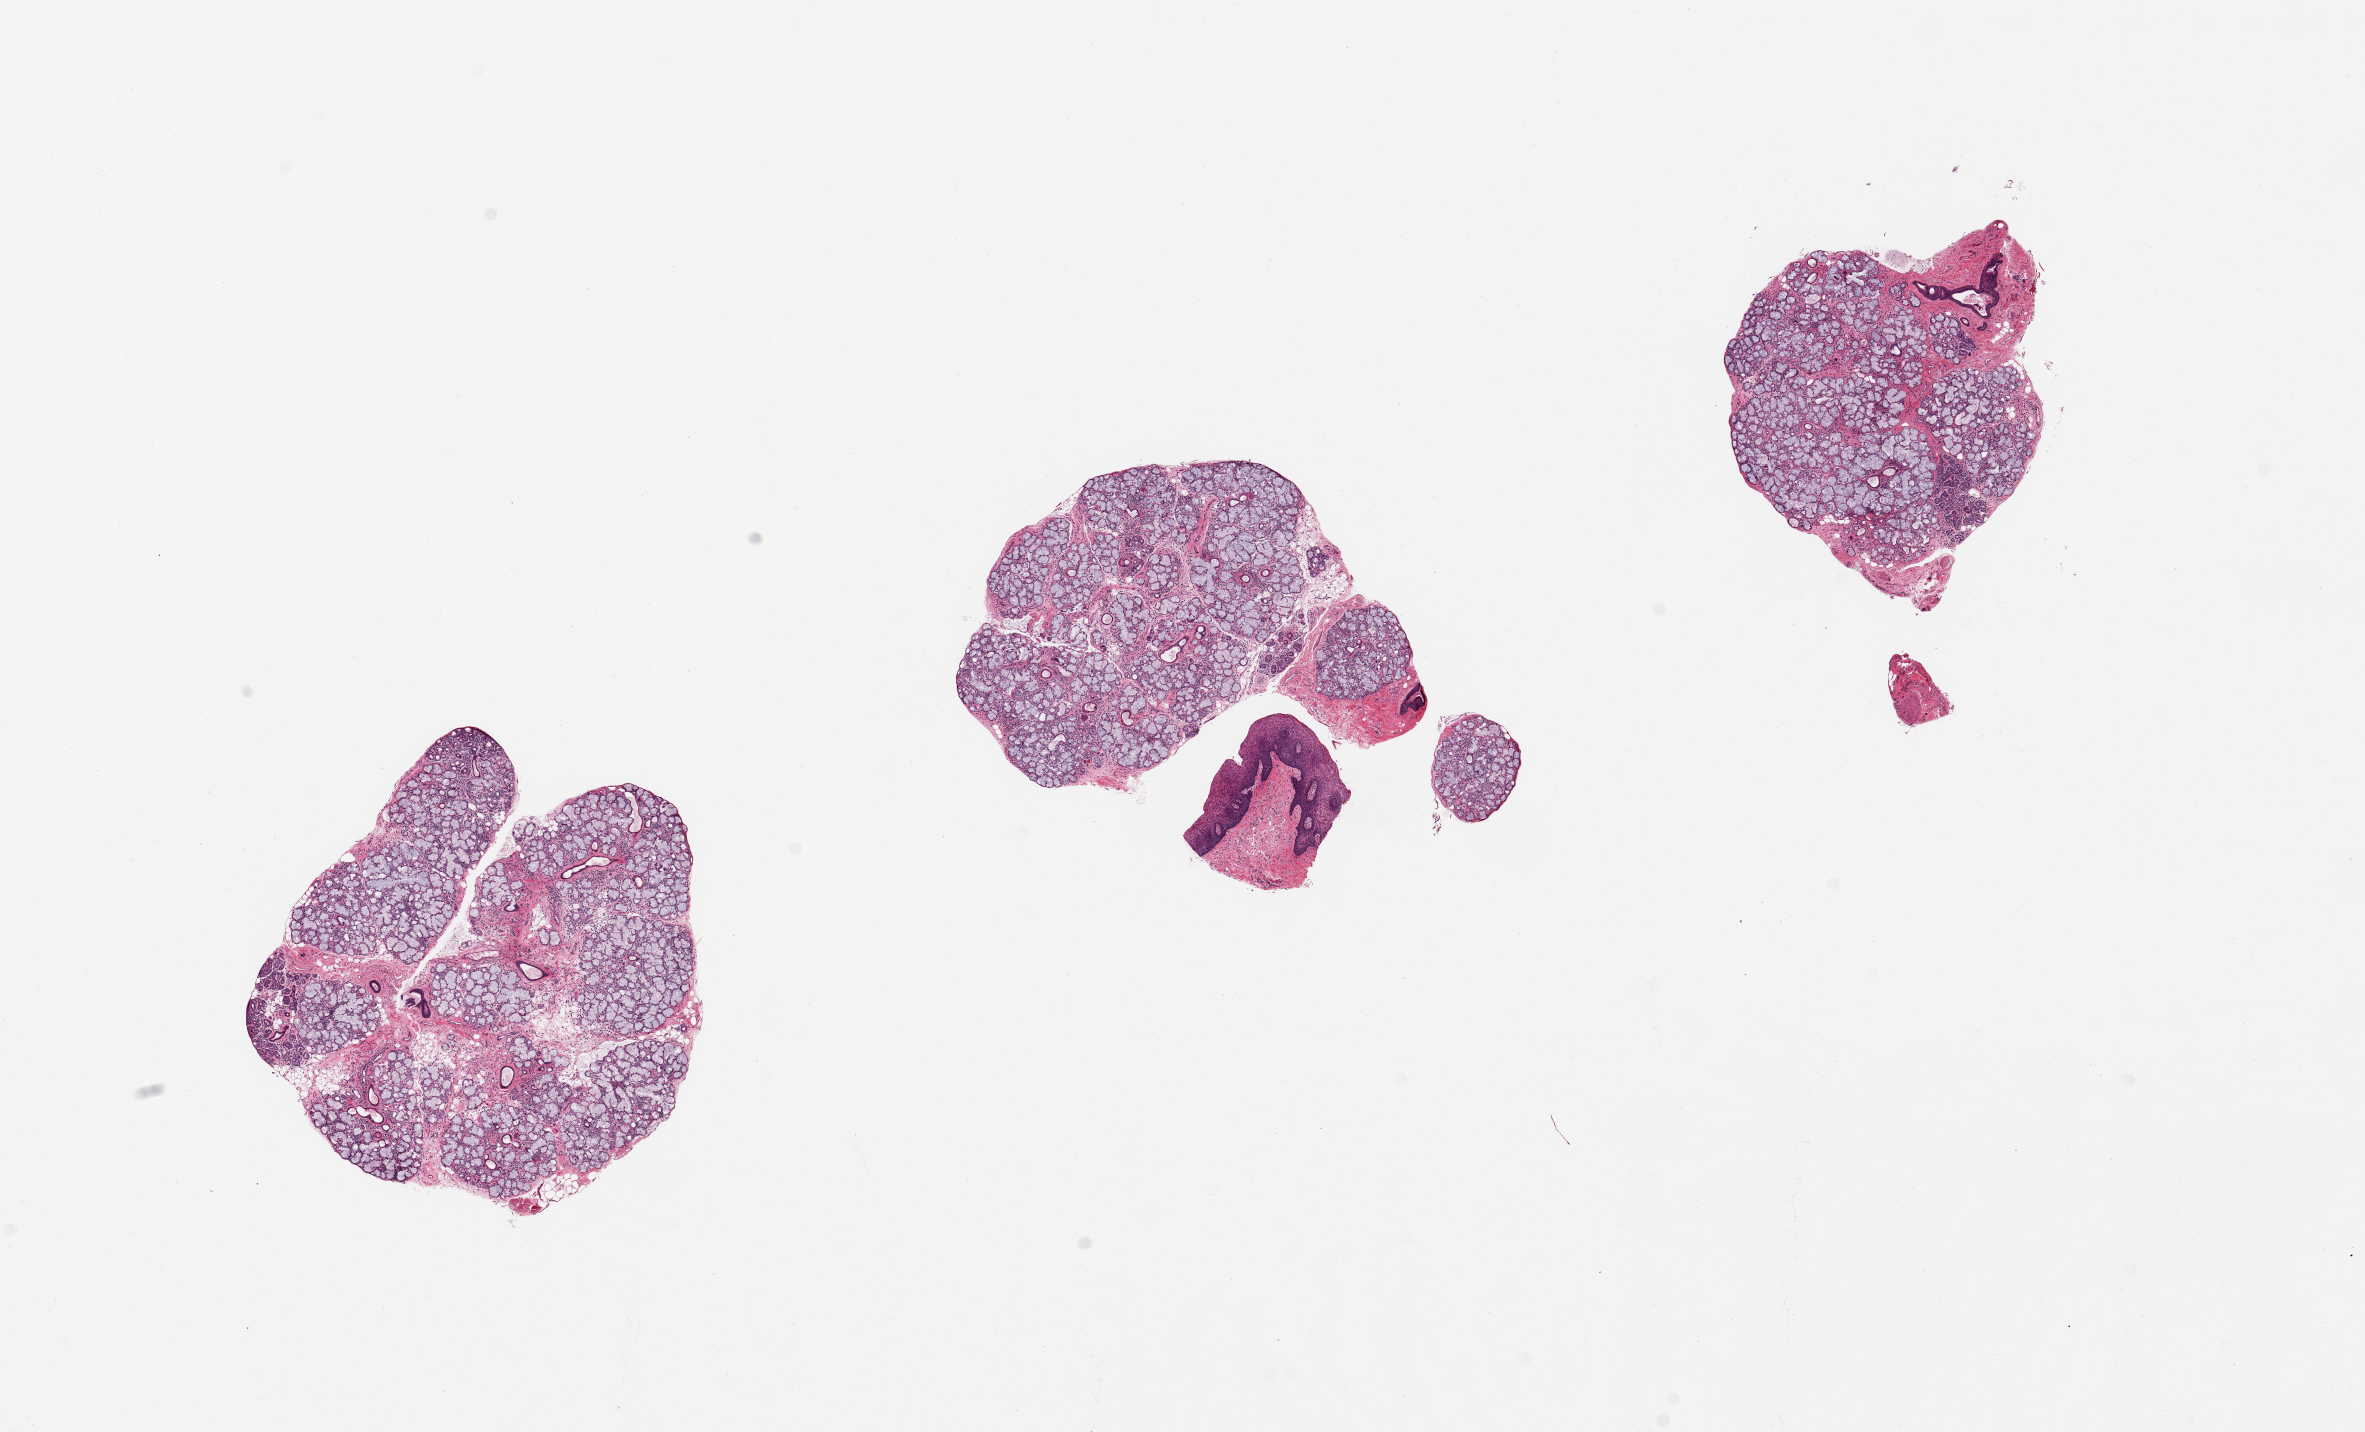
Whole-slide image, H&E stain, shown as a low-resolution overview of the whole scanned area (about 18.7 x 11.3 mm); PAXgene-fixed paraffin-embedded (PFPE) section; sampled site (target tissue): minor salivary gland; tissue donor sample. Donor: male.
Review note (as recorded): 3 pieces, up to 4x3.5mm; excellent specimens, well-preserved, 2mm nubbin non keratinizing squamous (inner lip) mucosa is present.